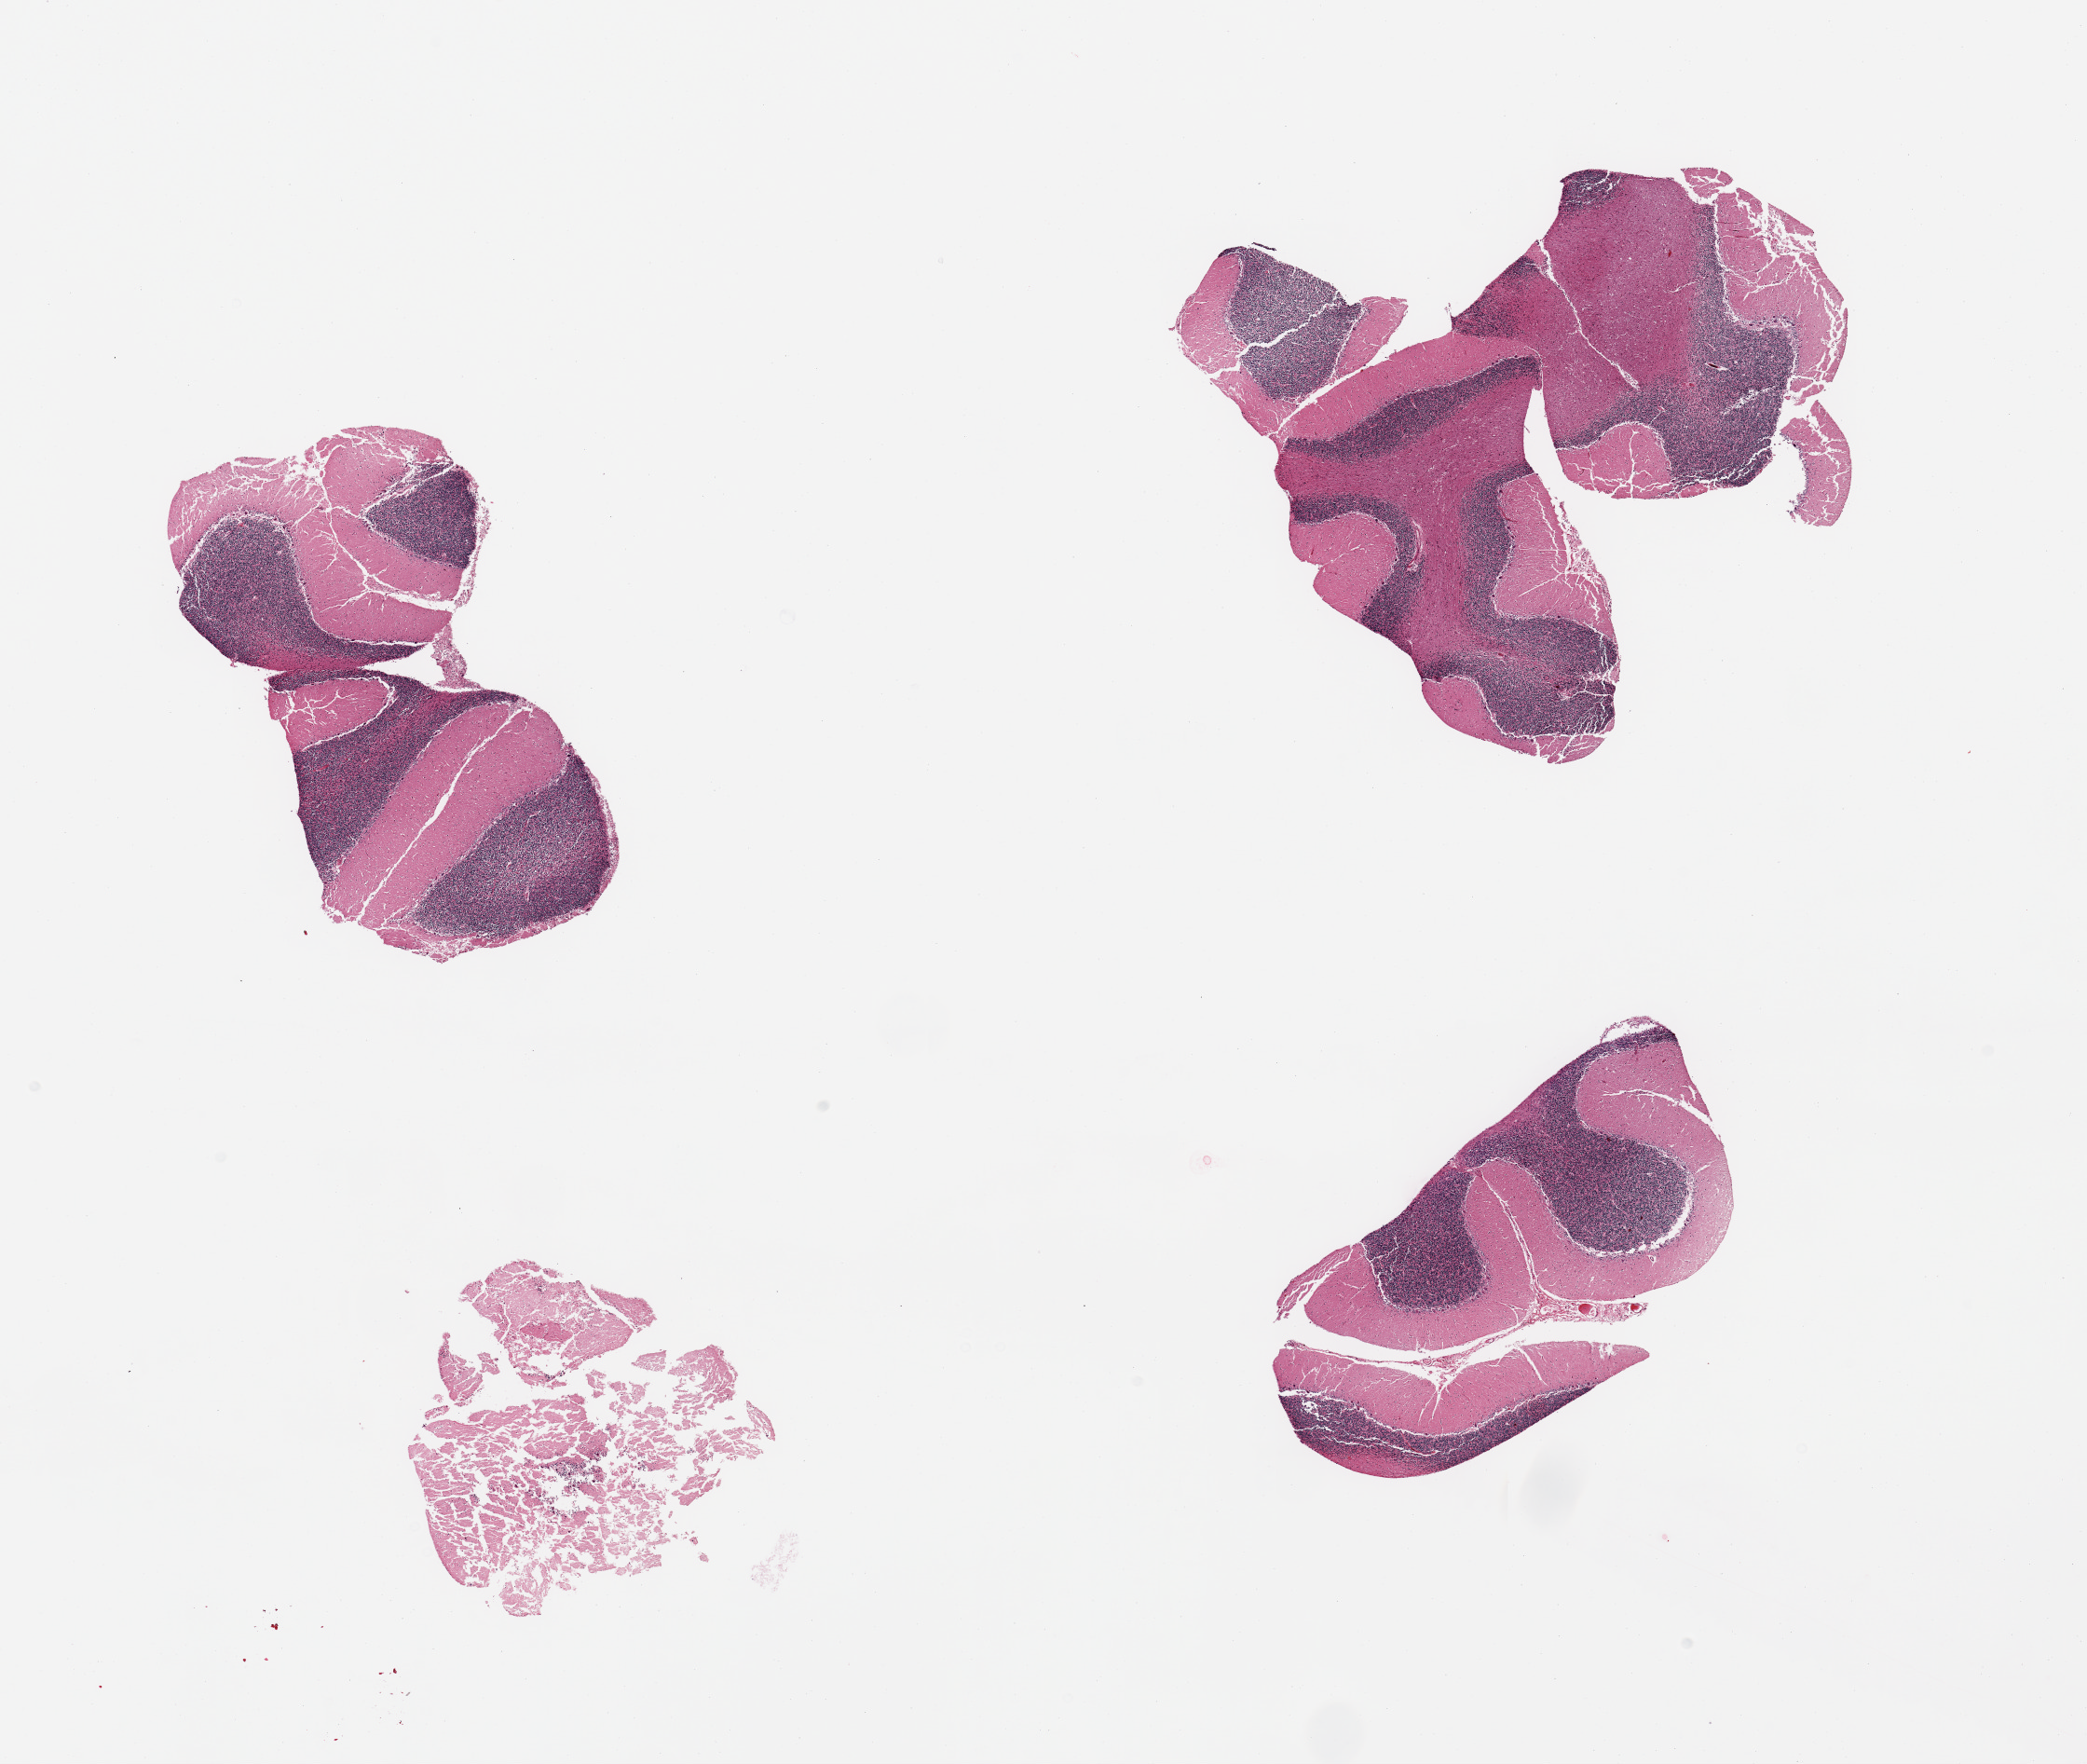
Haematoxylin and eosin whole-slide image, shown as a low-resolution overview of the whole scanned area (about 17.7 x 15.0 mm); PAXgene-fixed, paraffin-embedded tissue; sampled site (target tissue): cerebellum; donor tissue sample. Donor sex: male.
Review note (as recorded): 3 pieces, no abnormalities.